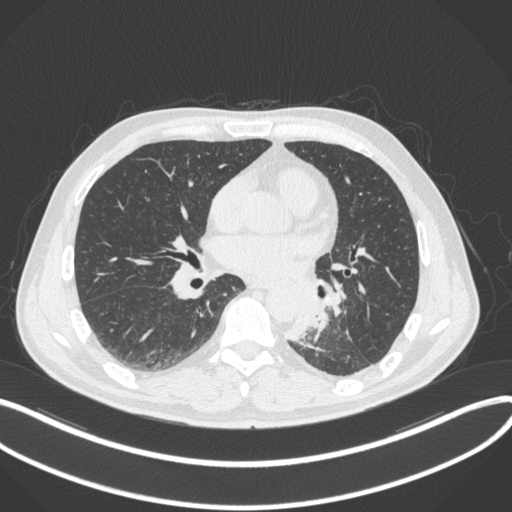
Chest CT, one axial slice. 120 kVp. Lung window (W 1500 / L -600 HU). 1 mm slice thickness. 512 × 512 image matrix, field of view 400 × 400 mm. Male patient, age 59 years. From the clinical record (not read from this slice): clinical TNM (as recorded): T2a N2 M0.
Annotated regions visible in this slice (rectangle marked by the reading radiologist):
- lung tumour (recorded histology: squamous cell carcinoma): box from (x=281, y=293) to (x=332, y=340) px